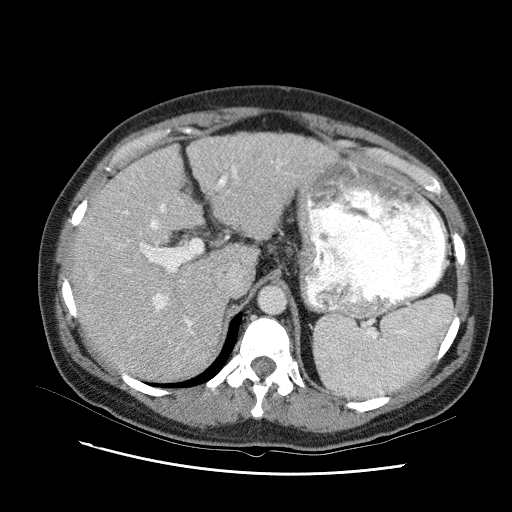
Contrast-enhanced abdominal CT (liver protocol), one axial slice. Slice 65 of 95 in the series (ordered by position). One of 2 acquisitions stored at this slice position. Soft-tissue window (W 400 / L 40 HU). 512 × 512 image matrix, field of view 360 × 360 mm. From the clinical record (not read from this slice): diagnosis: hepatocellular carcinoma (patient treated with transarterial chemoembolisation; whether this scan precedes or follows treatment is not stated here); TNM stage (as recorded): Stage-I; Child-Pugh class: B; tumour differentiation: moderately differentiated.
Annotated regions visible in this slice (semi-automatic segmentation, software-assisted and operator-edited):
- abdominal aorta: bounding box (x1, y1, x2, y2) in pixels: (259, 286, 284, 313)
- liver parenchyma outside the tumour (the mass and vessels are separate outlines, so this box may not span the whole liver): (68, 128, 339, 372)
- liver vessels: (107, 151, 304, 355)